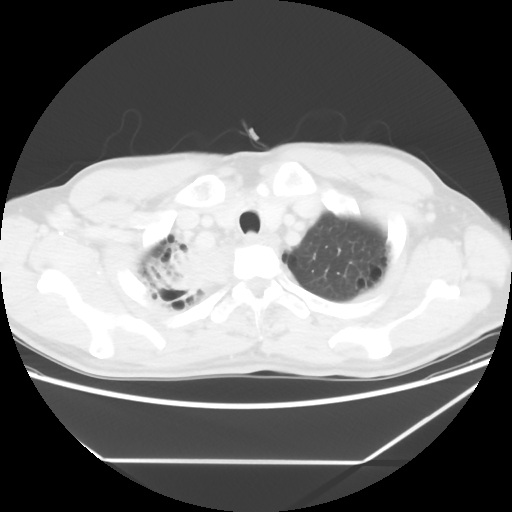
Chest CT, one axial slice. Position 54 of 60 along the scan axis. Reconstruction kernel STANDARD. Lung window (W 1500 / L -600 HU). 5 mm slice thickness. 512 × 512 image matrix. Patient: male, 58 years. From the clinical record (not read from this slice): clinical TNM (as recorded): T2 N2 M0.
Outlined on this slice (rectangle marked by the reading radiologist):
- lung tumour (recorded histology: squamous cell carcinoma): box from (x=155, y=239) to (x=230, y=301) px